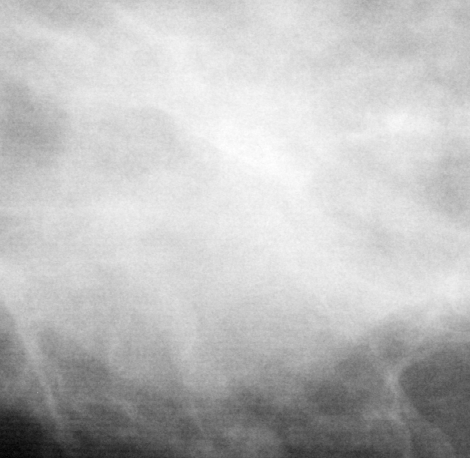
Crop from a digitized film mammogram around one marked abnormality; left breast; MLO view; BI-RADS breast density category 1 (scale 1–4).
Mass, shape lobulated, margins microlobulated; BI-RADS assessment category 5; subtlety rating 5 on a 1 (subtle) to 5 (obvious) scale; pathology (as recorded): malignant.